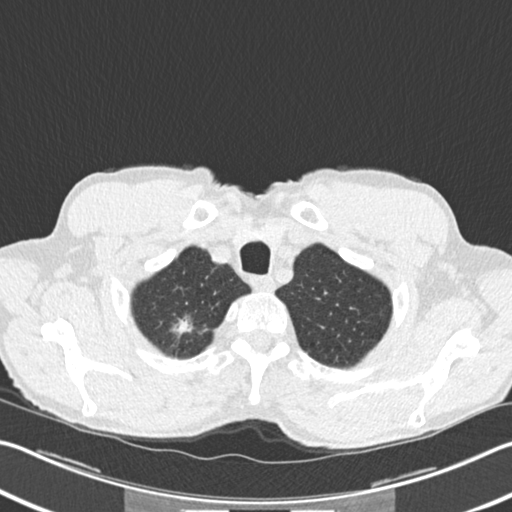
Low-dose screening chest CT, one axial slice; 120 kVp; lung window (W 1500 / L -600 HU); 2 mm slice thickness; 512 × 512 image matrix.
Annotated regions visible in this slice (expert manual segmentation):
- lesion 1 (tumor, upper lobe of right lung): bounding box (x1, y1, x2, y2) in pixels: (172, 317, 192, 336)